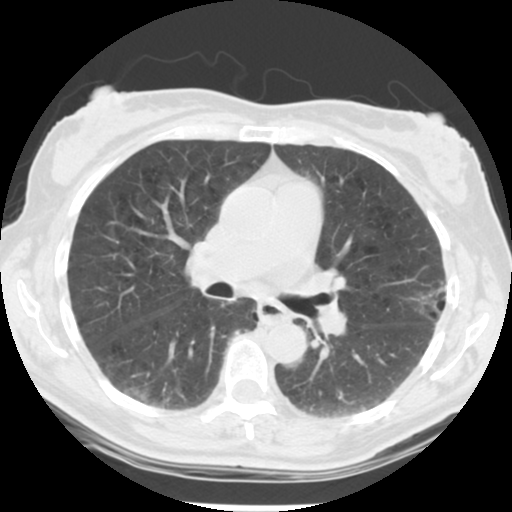
Axial slice from a low-dose chest CT screening exam, second screening round (one year after baseline), lung window (W 1500 / L -600 HU), 2.5 mm slice thickness, standard (soft-tissue) reconstruction kernel (STANDARD), slice 126 of 223 in the series, 512 × 512 image matrix. Female, age 61 years at enrolment. Current smoker at enrolment.
Expert reader's lesion annotation, bounding box (x1, y1, x2, y2) in pixels: (402, 271, 464, 331). The exam's reader record, not a measurement of the box and not confirmed to be the same lesion: non-calcified nodule or mass ≥4 mm, left upper lobe, 15 × 15 mm, poorly defined margins, mixed attenuation, pre-existing on the prior screen: no. Official screen result: positive, other. Later outcome: lung cancer diagnosed 152 days after this screen — bronchiolo-alveolar adenocarcinoma, NOS, left upper lobe, well differentiated (G1), stage IA (AJCC 6th edition), 11 mm at pathology.